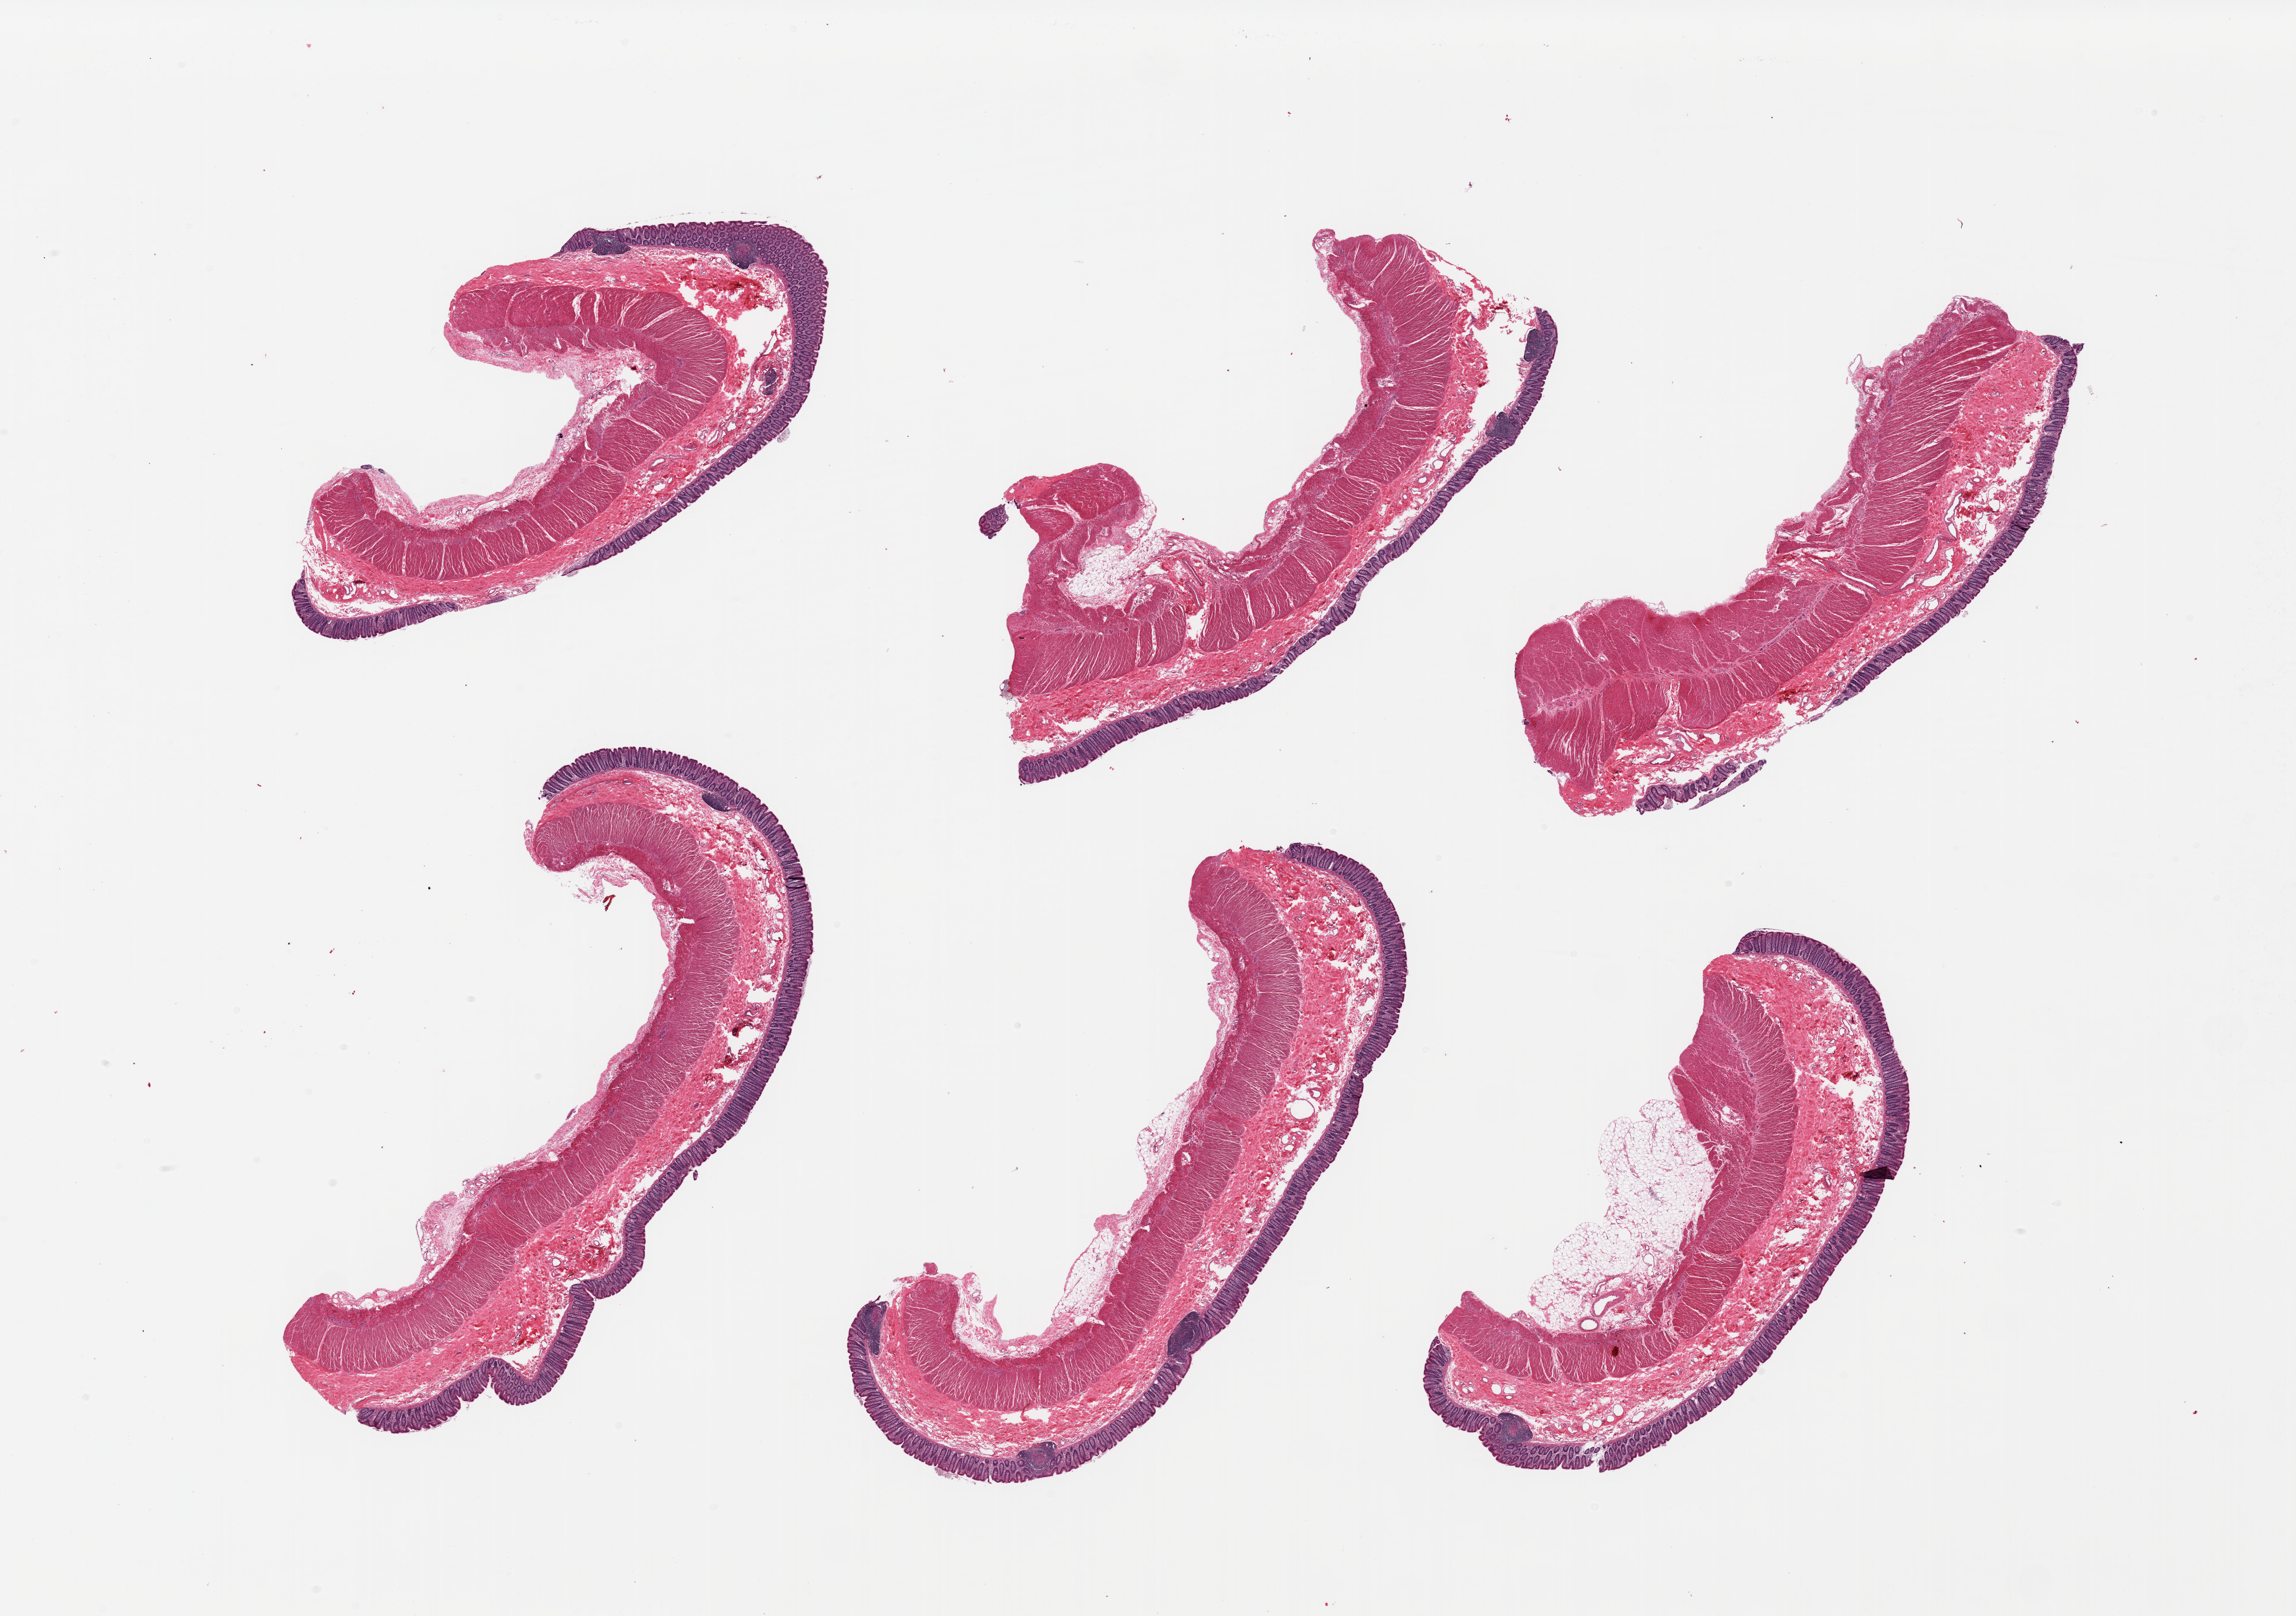
Digitized hematoxylin and eosin (H&E)-stained section, brightfield — a low-resolution overview of the entire scanned area, about 31.5 x 22.2 mm (from a 20x scan); PAXgene-fixed, paraffin-embedded tissue; target tissue: transverse colon; donor tissue sample. Female donor.
* review note (as recorded): 6 pieces; full thickness sections